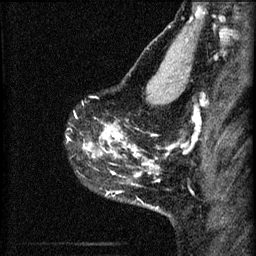
Breast MRI (dynamic contrast-enhanced), one sagittal slice. Position 45 of 60 along the scan axis. 3 images stored at this slice position (order not interpretable as contrast timing). 1.5 T. TE 4.2 ms, TR 8.2 ms. 2 mm slice thickness. 256 × 256 image matrix, field of view 180 × 180 mm. Female patient, age 40 years.
Structures marked on this image (semi-automatically segmented with operator editing):
- analysis volume of interest (the breast-tissue region the enhancement analysis was run in; not a lesion): bounding box (x1, y1, x2, y2) in pixels: (68, 76, 179, 215)
- tumour enhancement mask (voxels above the 70 % enhancement threshold inside the analysis volume of interest): (84, 124, 153, 177)